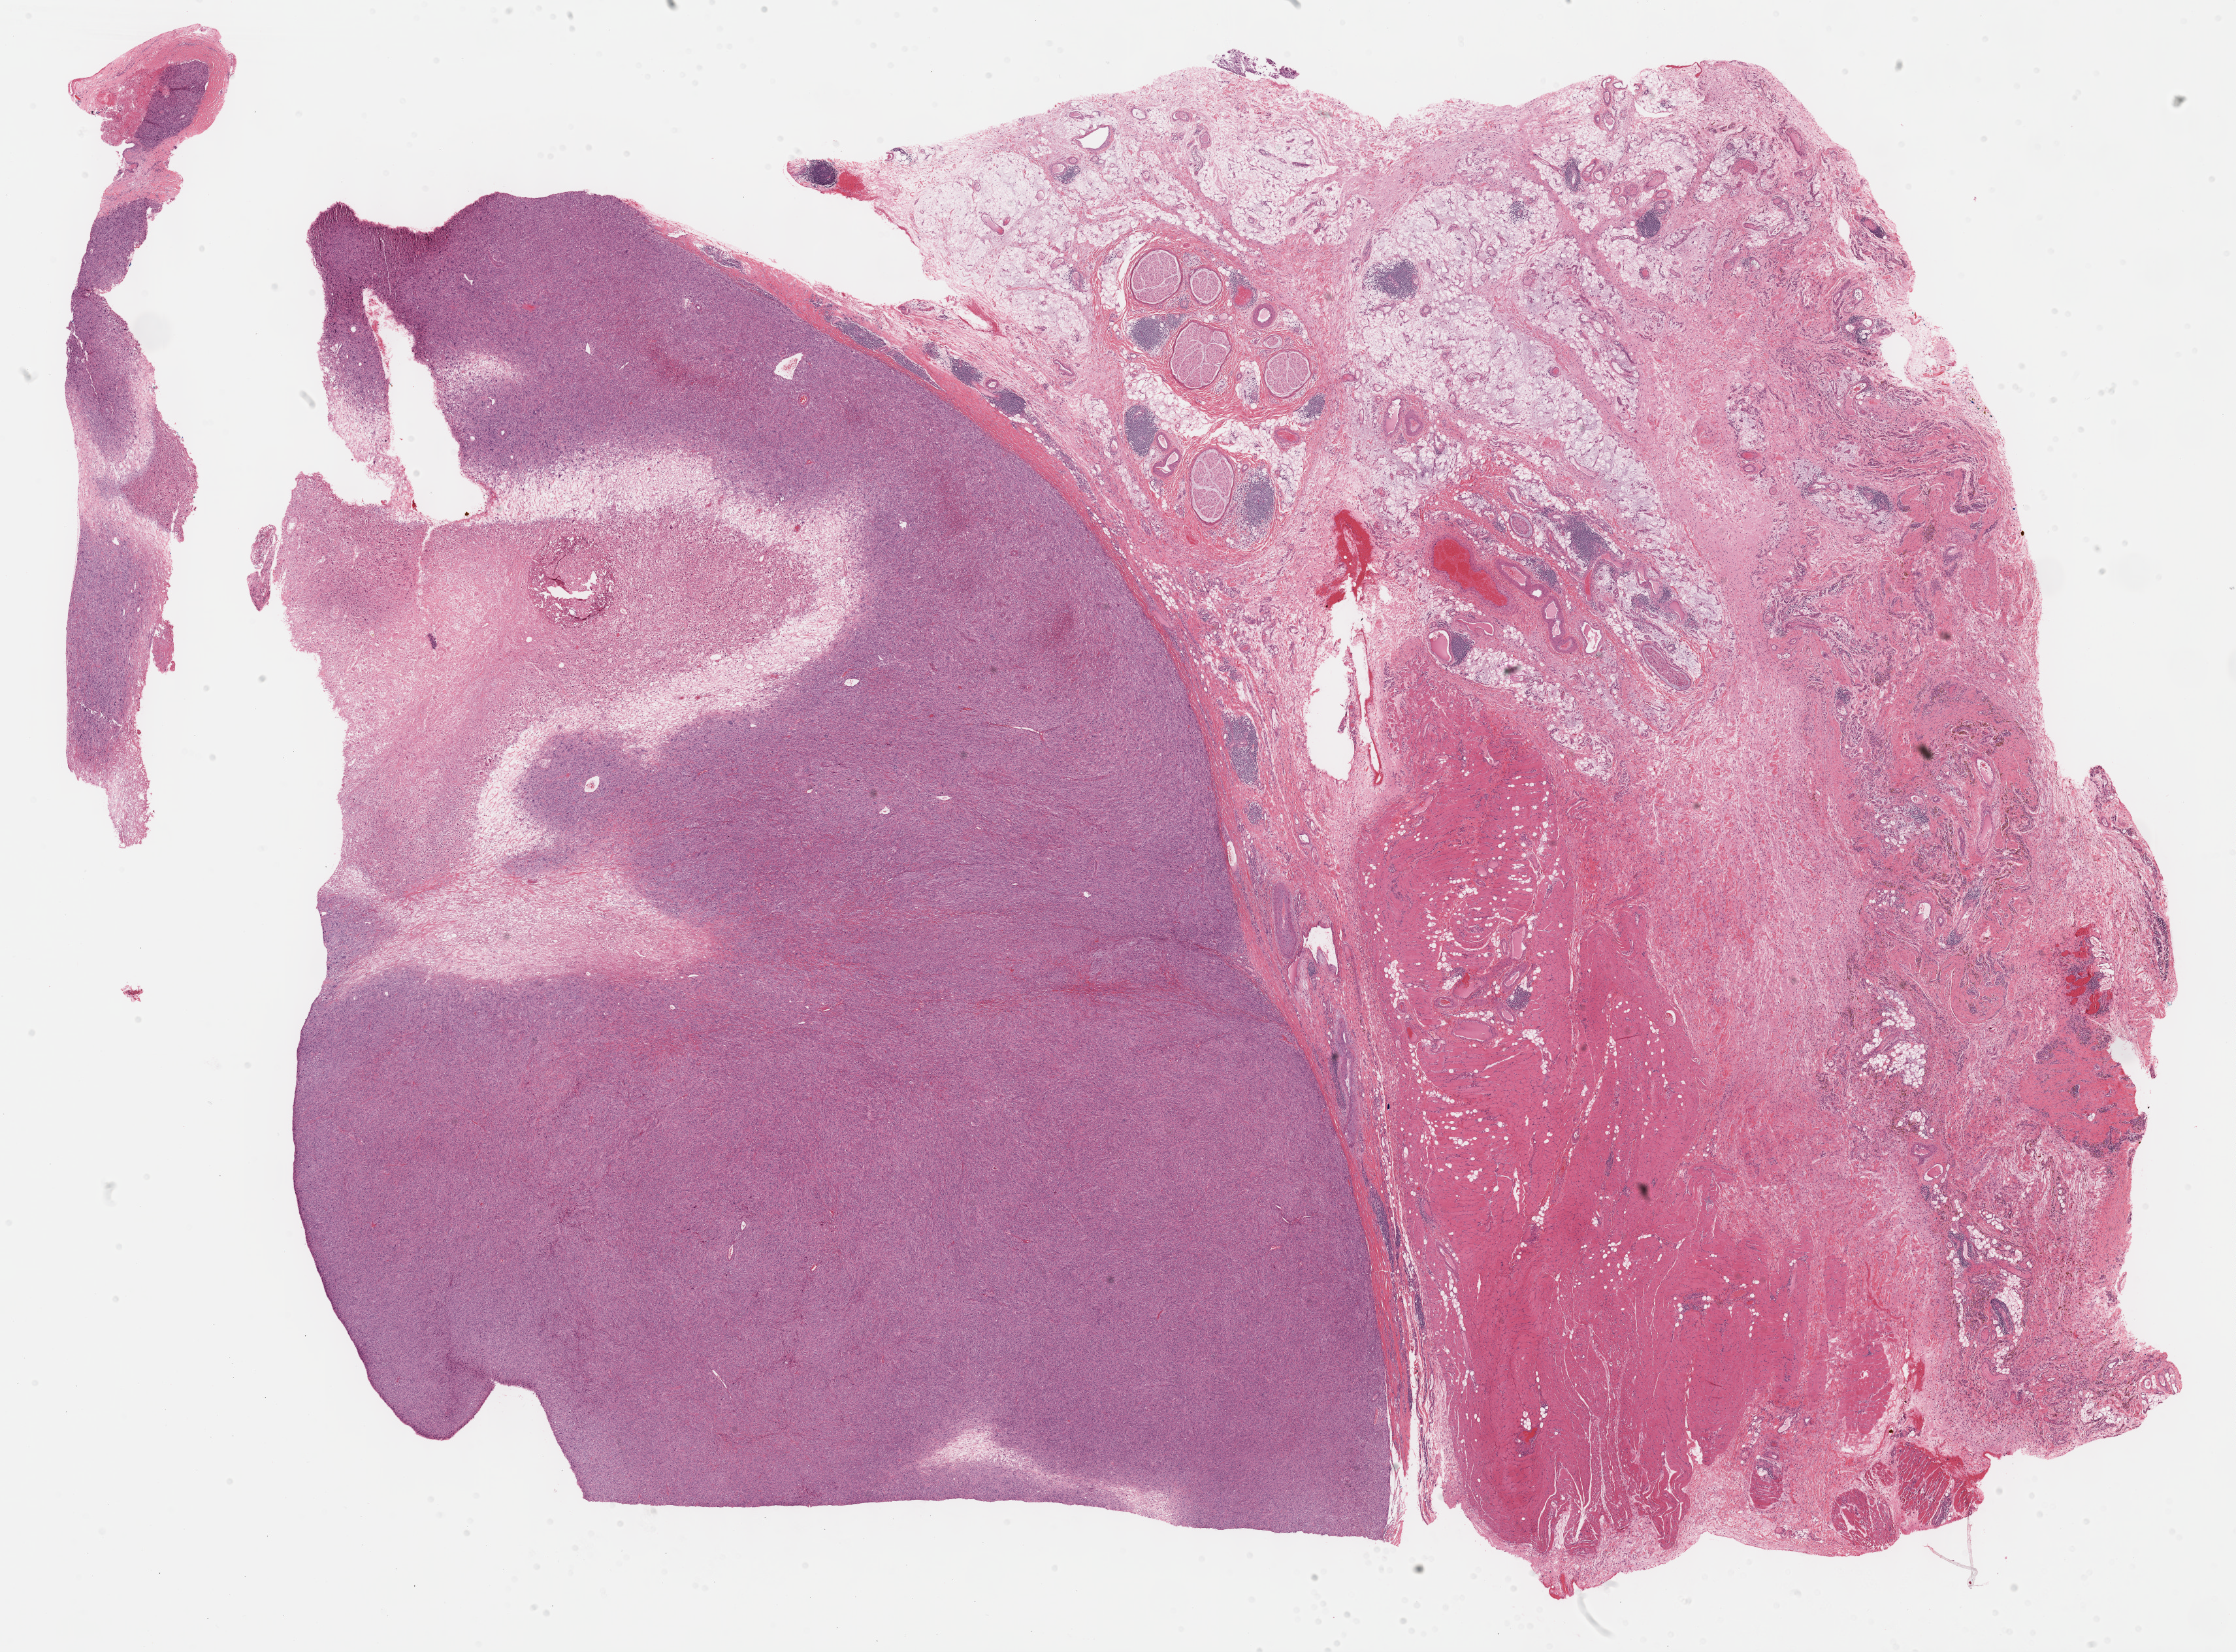
H&E whole-slide image, low-resolution overview of the scanned area, about 27.7 x 20.5 mm. FFPE section. Primary tumour sample from the connective, subcutaneous and other soft tissues. Female patient; age at initial diagnosis 62 years.
Histologic diagnosis: Malignant fibrous histiocytoma (connective, subcutaneous and other soft tissues of lower limb and hip).